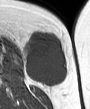
MRI of an extremity soft-tissue mass, one axial slice. Position 15 of 45 along the scan axis. MR volume resampled by the dataset authors to the PET/CT grid (not the native acquisition matrix). 90 × 109 image matrix, field of view 88 × 106 mm. Female patient. From the clinical record (not read from this slice): histological type: leiomyosarcoma; grade: intermediate; site of the primary tumour: parascapusular.
Annotated regions visible in this slice (expert contour drawn on MRI and transferred to this co-registered scan by the dataset authors):
- gross tumour volume including surrounding oedema: box from (x=24, y=32) to (x=68, y=86) px
- gross tumour volume (mass): (x=24, y=32)–(x=68, y=86)